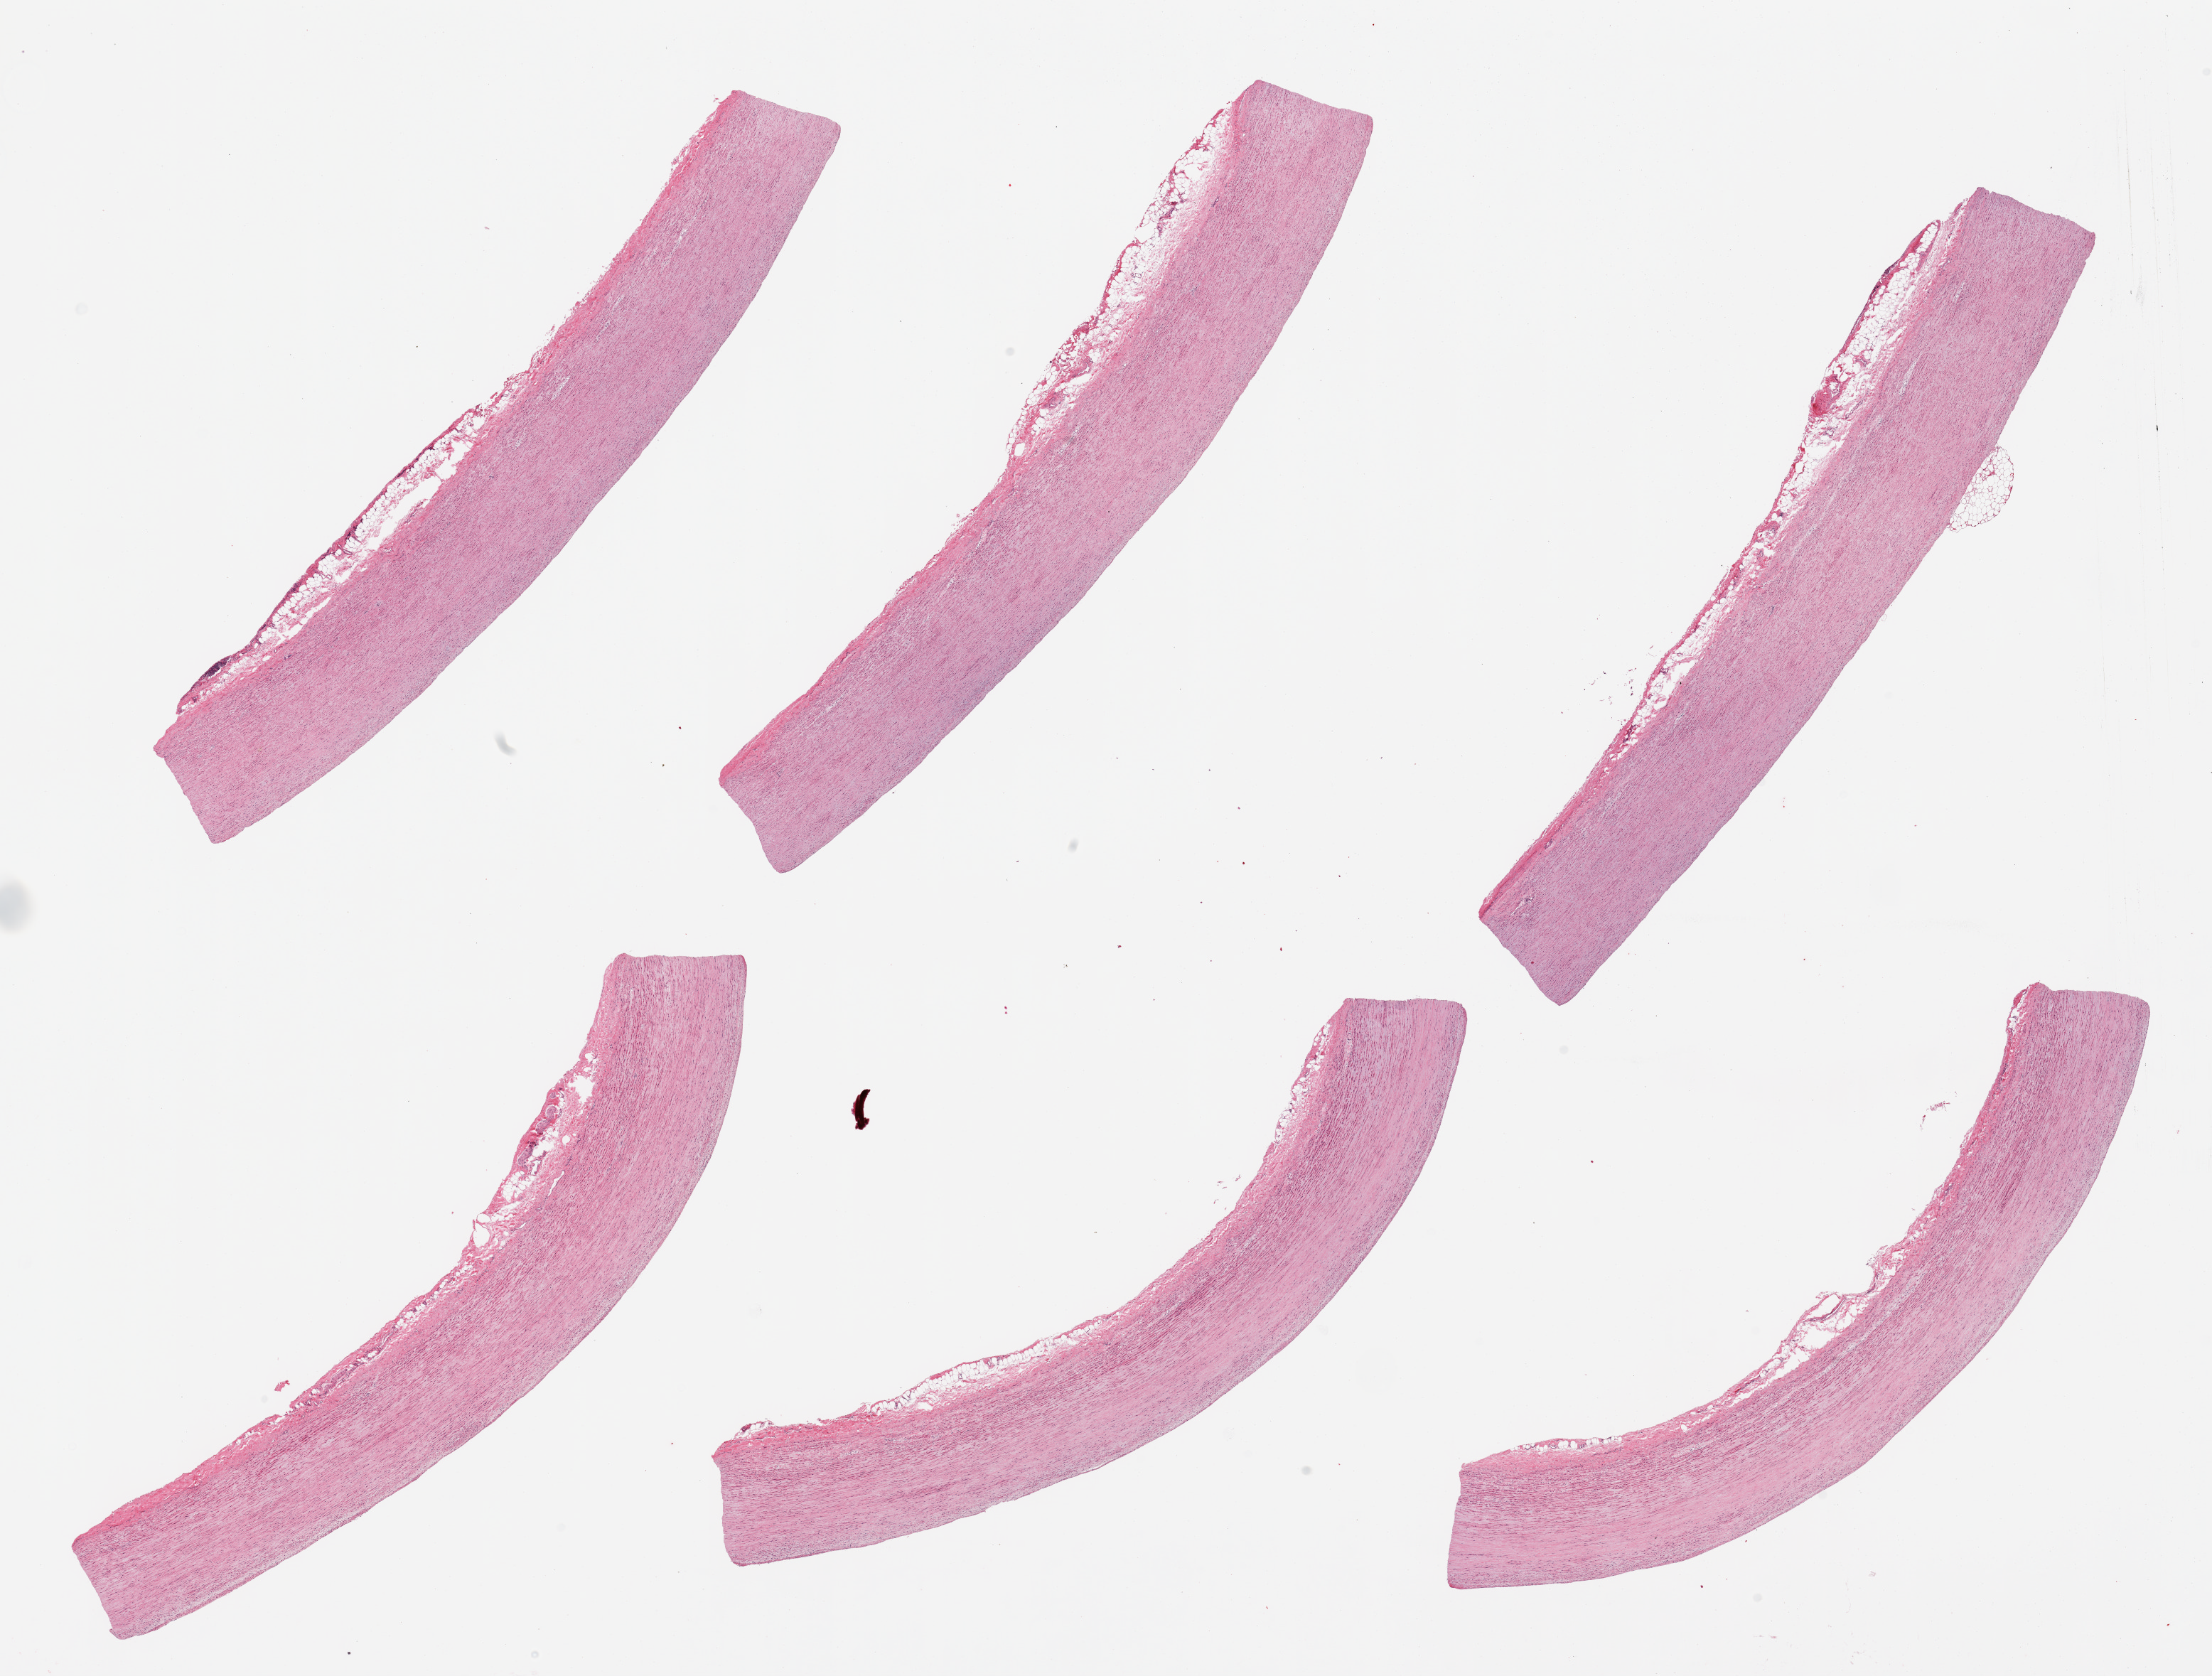
H&E whole-slide image, low-resolution overview of the scanned area, about 24.6 x 18.6 mm (acquisition: 20x scan), PAXgene-fixed, paraffin-embedded tissue, section of aorta (target tissue), donor tissue sample.
Reviewer comment on this tissue sample: 6 pieces, minimal atherosis.